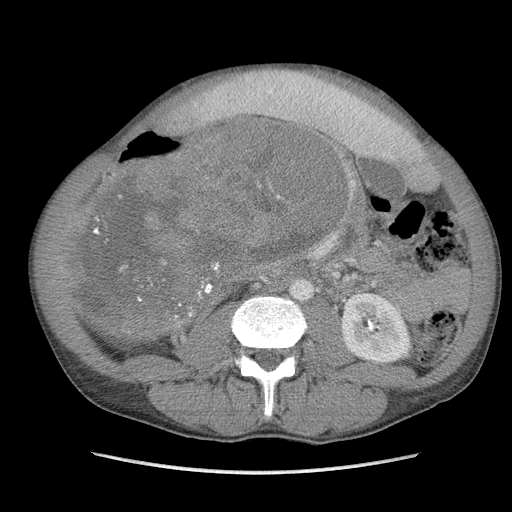
Contrast-enhanced abdominal CT, one axial slice; slice 48 of 115 in the series (ordered by position); soft-tissue window (W 400 / L 40 HU); 5 mm slice thickness; 512 × 512 image matrix. Male patient. From the clinical record (not read from this slice): diagnosis: adrenocortical carcinoma; tumour side: right adrenal; Ki-67 index: 13 %; stage (as recorded): 3.
Structures marked on this image (semi-automatic segmentation, software-assisted and operator-edited):
- mass: bounding box <79,121,341,328> (left, top, right, bottom; pixels)